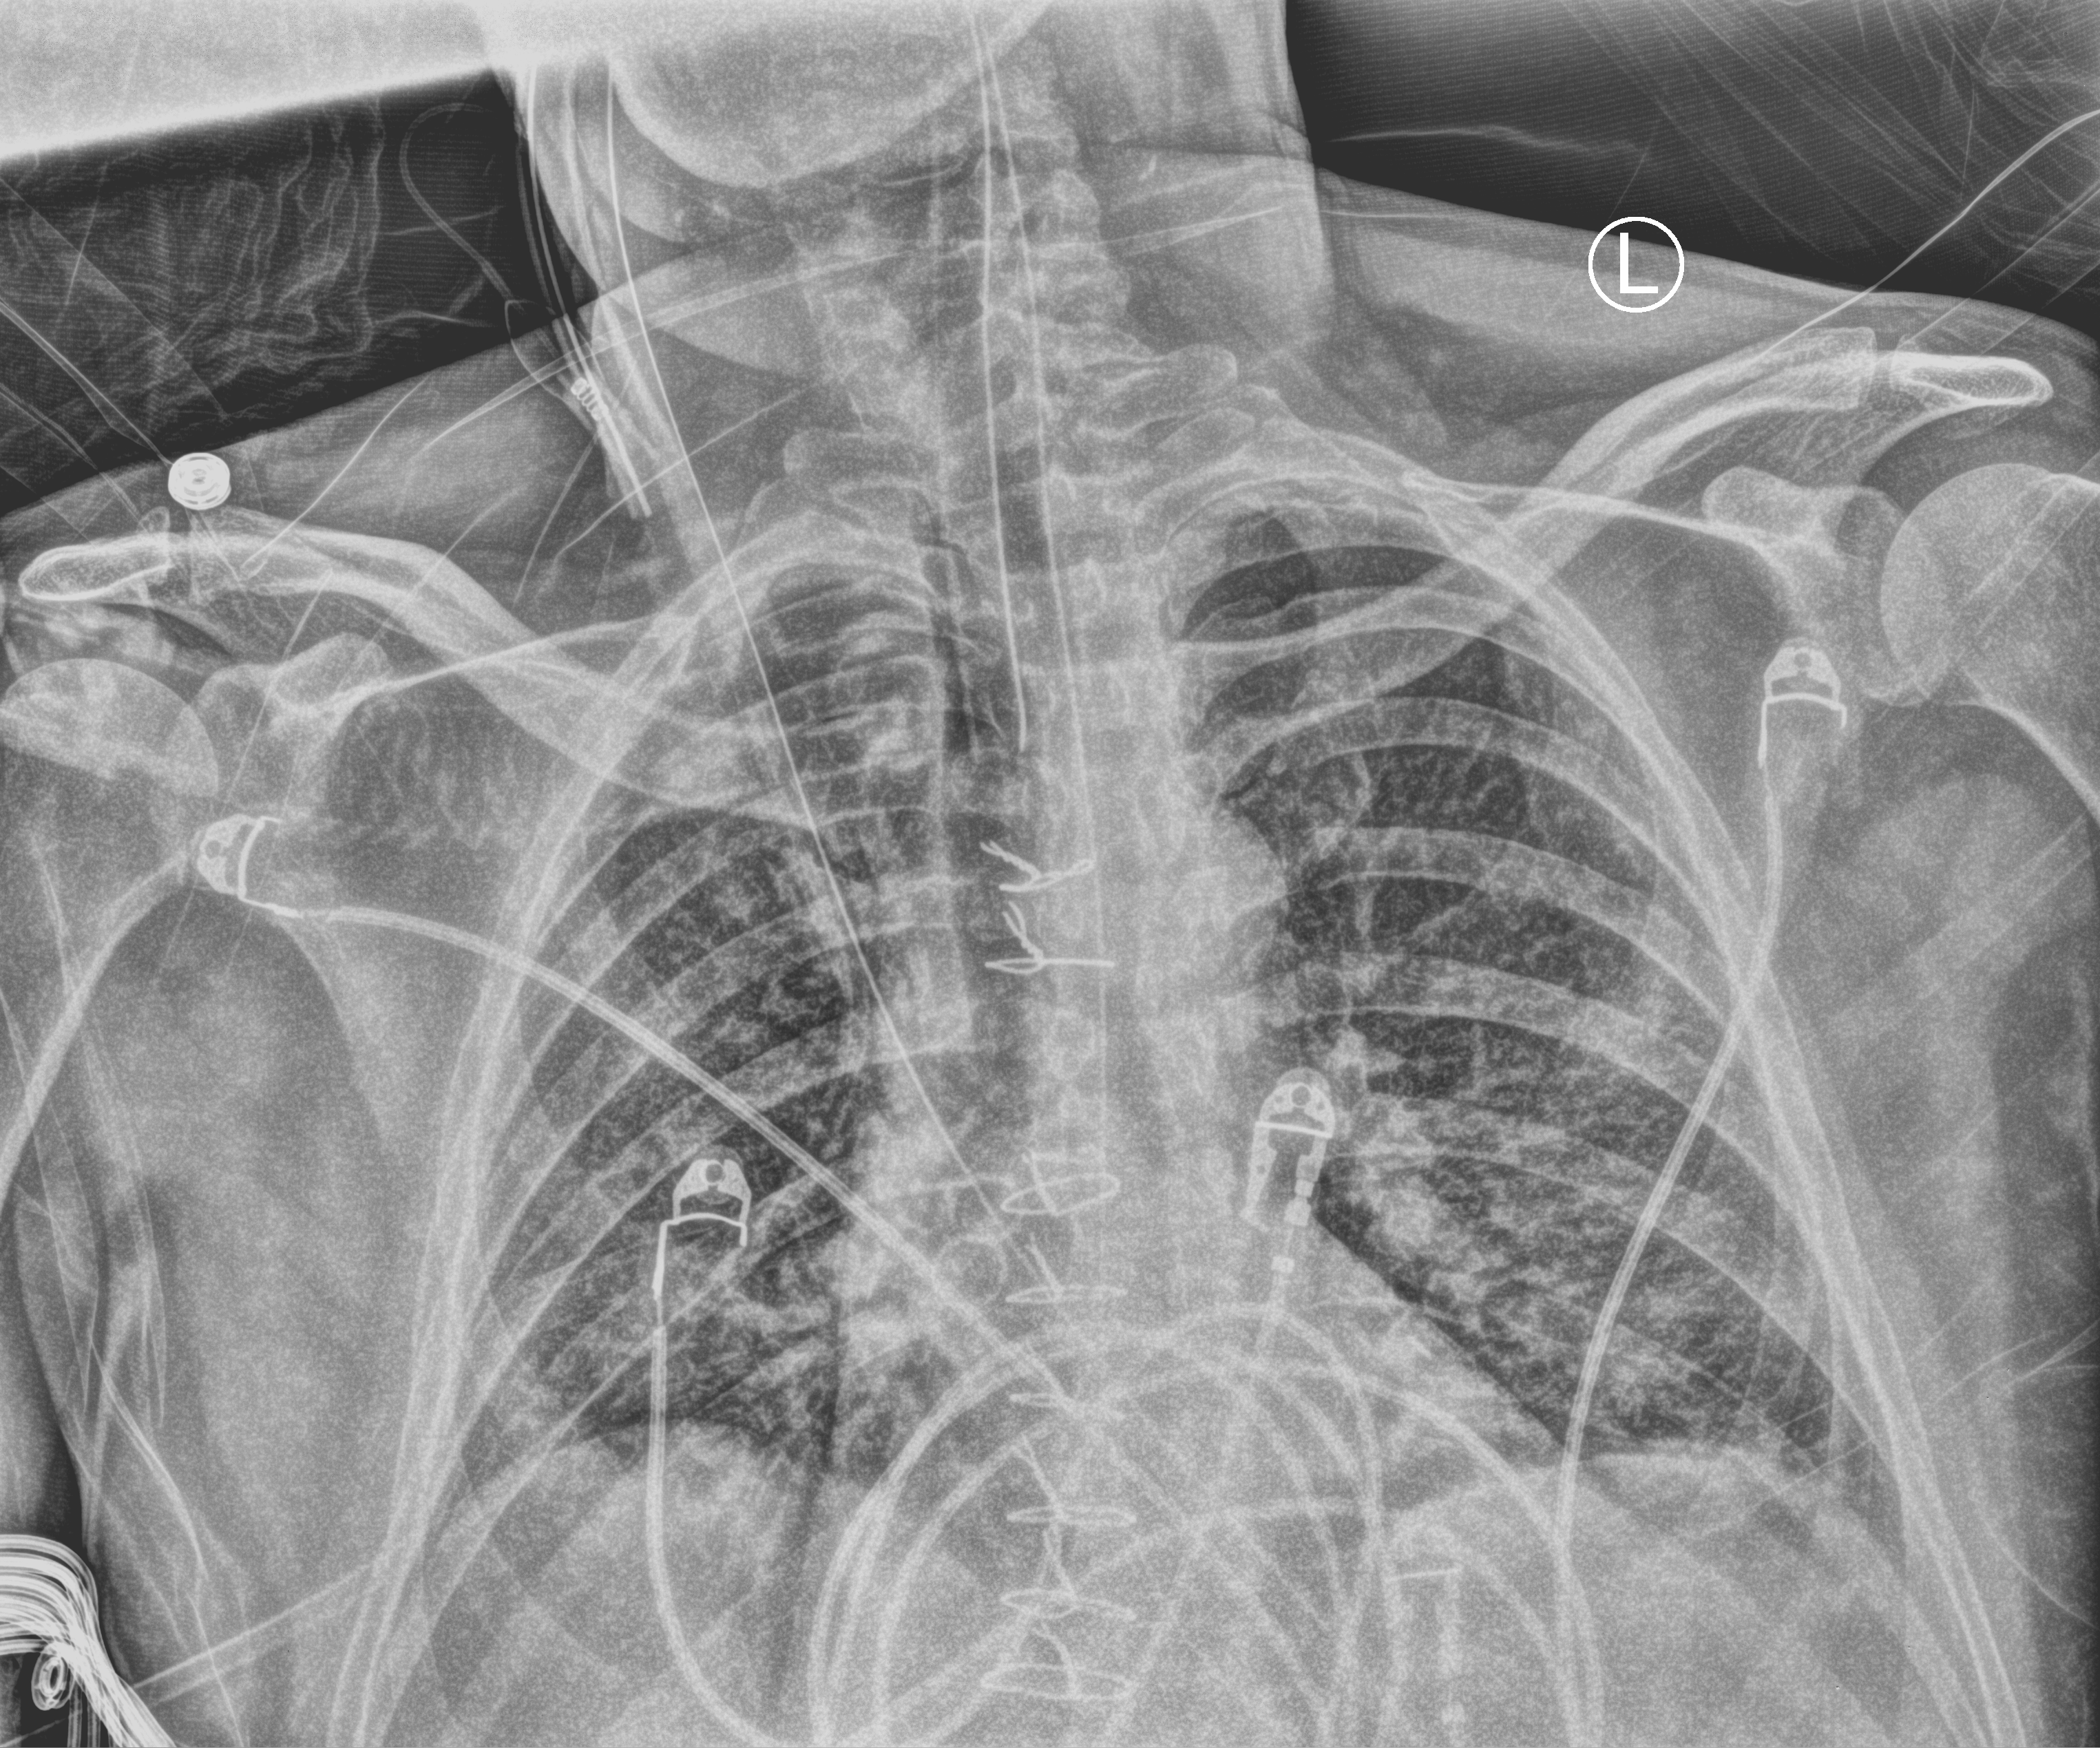
Portable chest radiograph; anteroposterior (AP) projection. Patient hospitalised with COVID-19; male, aged 18–59 years.
Admission-level facts for this patient (not findings on this image; timing relative to this image not recorded): hypertension (admission record): no; mechanically ventilated during this hospital stay: yes; admitted to intensive care during this hospital stay: yes.